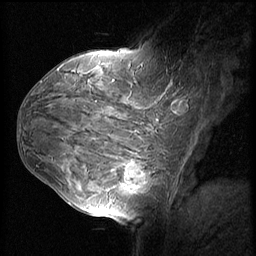
Breast MRI (dynamic contrast-enhanced), one sagittal slice. Slice 35 of 60 in the series (ordered by position). Dynamic contrast-enhanced series, image 2 of 3 at this slice position (ordered by acquisition). 1.5 T. TE 4.2 ms, TR 8.9 ms. 2.5 mm slice thickness. 256 × 256 image matrix. Female patient, age 37 years. From the clinical record (not read from this slice): setting: breast cancer imaged before/during neoadjuvant chemotherapy; receptor status: triple-negative.
Structures marked on this image (semi-automatically segmented with operator editing):
- analysis volume of interest (the breast-tissue region the enhancement analysis was run in; not a lesion): box from (x=114, y=153) to (x=159, y=206) px
- tumour enhancement mask (voxels above the 140 % enhancement threshold inside the analysis volume of interest): (x=122, y=164)–(x=147, y=192)